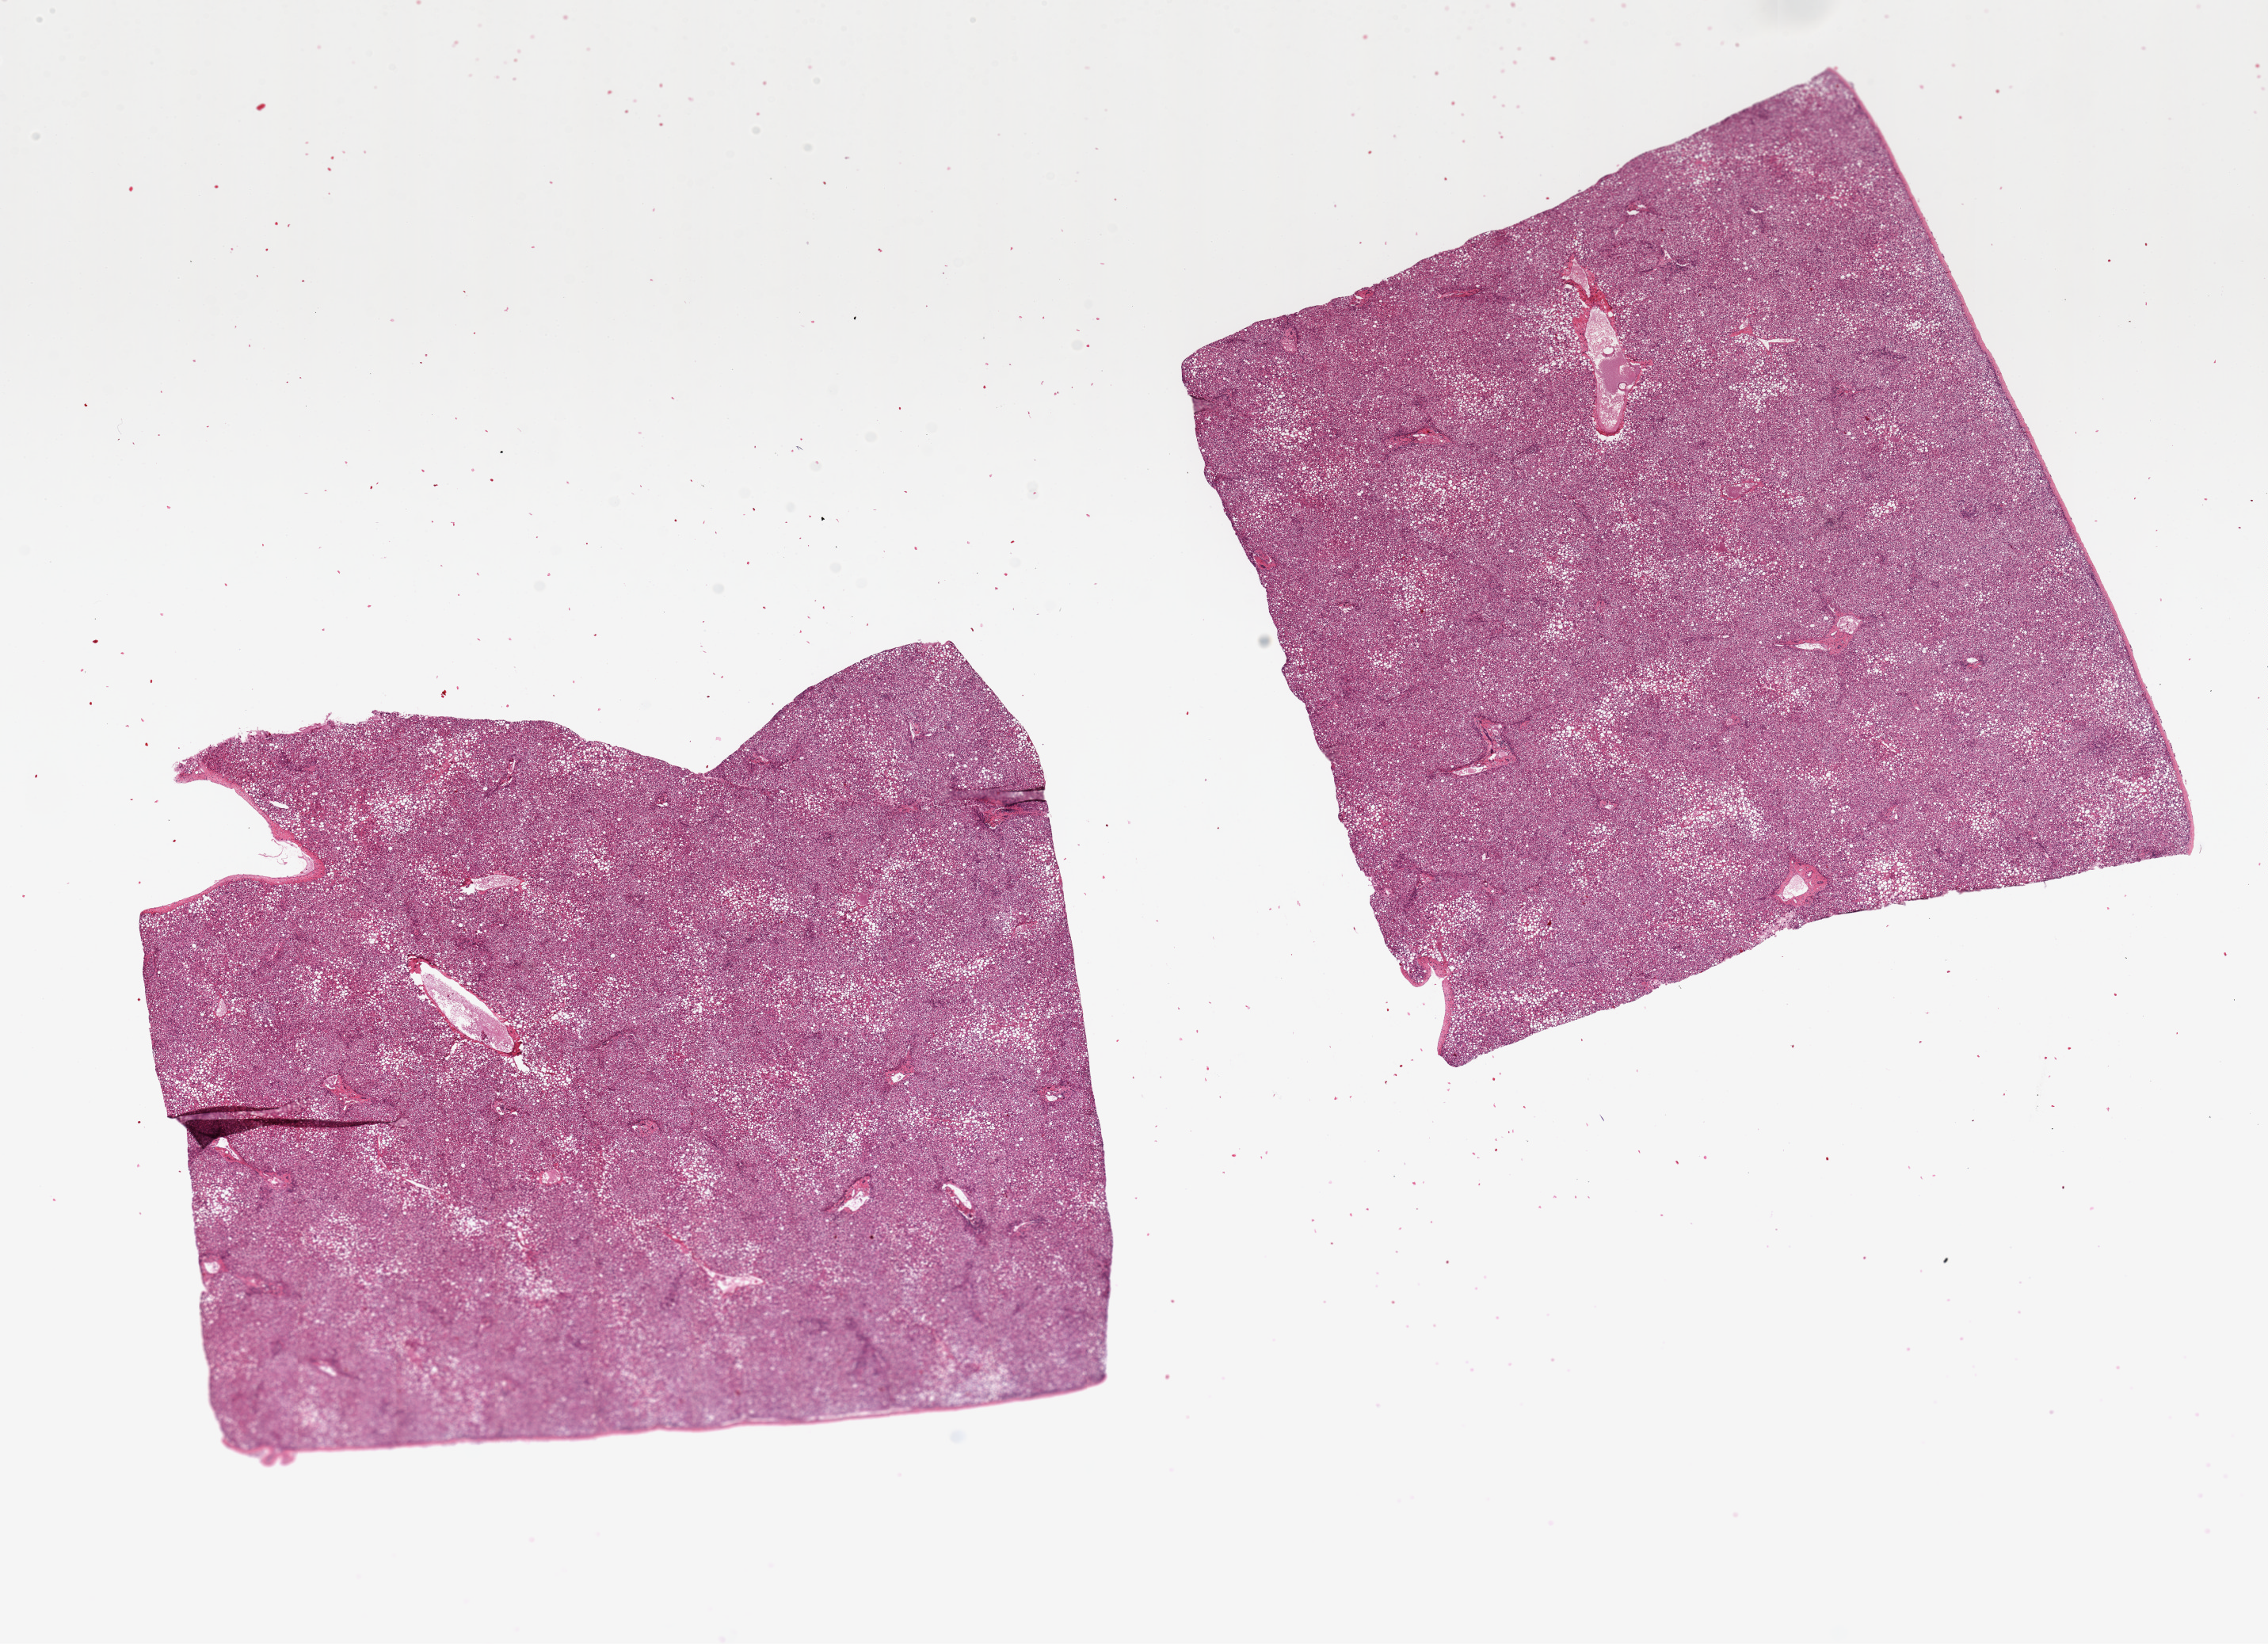
Whole-slide image, H&E stain — a low-resolution overview of the entire scanned area, about 22.6 x 16.4 mm (slide scanned at 20x); PAXgene-fixed, paraffin-embedded tissue; section of liver (target tissue); tissue donor sample. Male donor.
Reviewer comment on this tissue sample: 2 pieces ~9x7mm, 90% macrovesicular steatosis but reasonably well preserved.